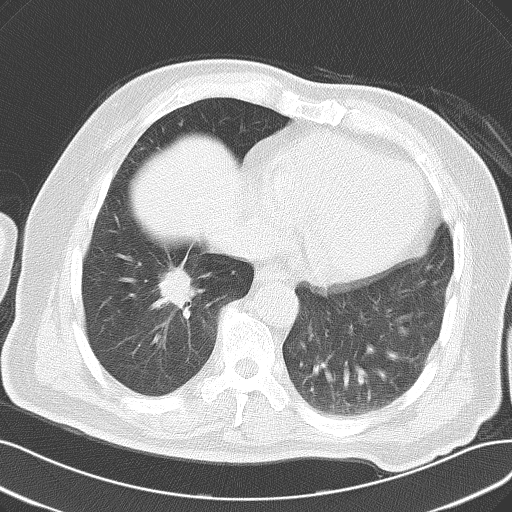
Chest CT, one axial slice; slice 25 of 61 in the series (ordered by position); reconstruction kernel B70f; lung window (W 1500 / L -600 HU); 5 mm slice thickness; 512 × 512 image matrix. Patient: male, 69 years. Case-level facts recorded for this patient, not image findings: clinical TNM (as recorded): T1c N0 M0; histopathological grade: G2-3.
Outlined on this slice (rectangle marked by the reading radiologist):
- lung tumour (recorded histology: adenocarcinoma): box from (x=157, y=263) to (x=199, y=315) px